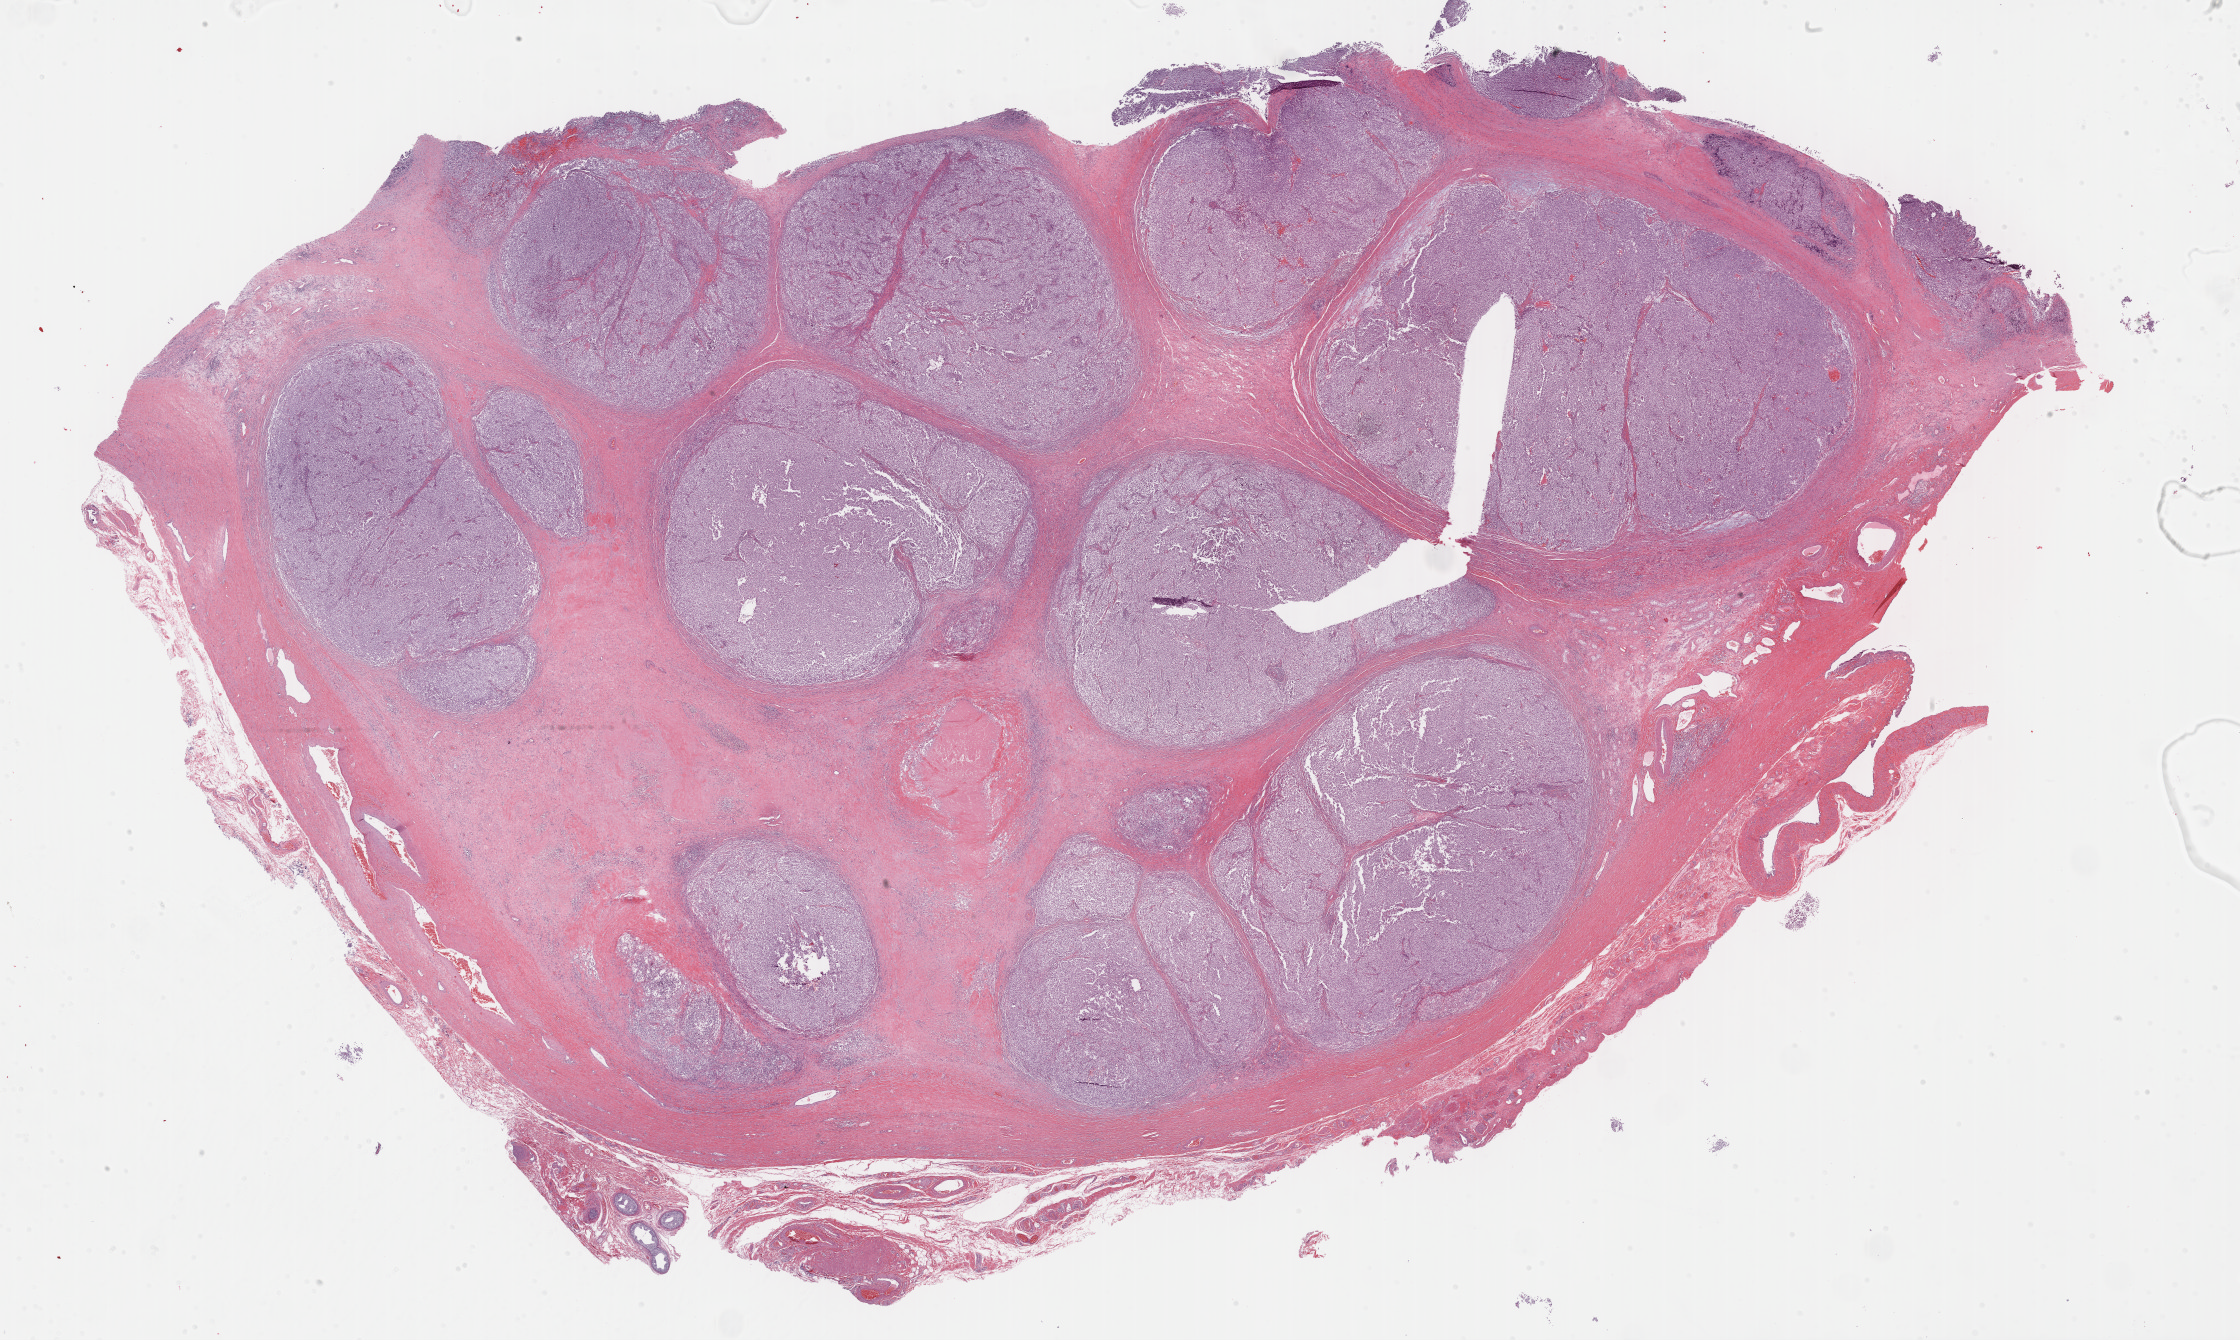
H&E whole-slide image — whole scanned area (about 36.2 x 21.7 mm, slide scanned at 40x) shown as a low-resolution overview; FFPE section; primary tumour sample from the testis. Patient: male, age at initial diagnosis 35 years.
Diagnosis: Seminoma, NOS. Laterality: right. AJCC pathologic stage: IA (6th edition).